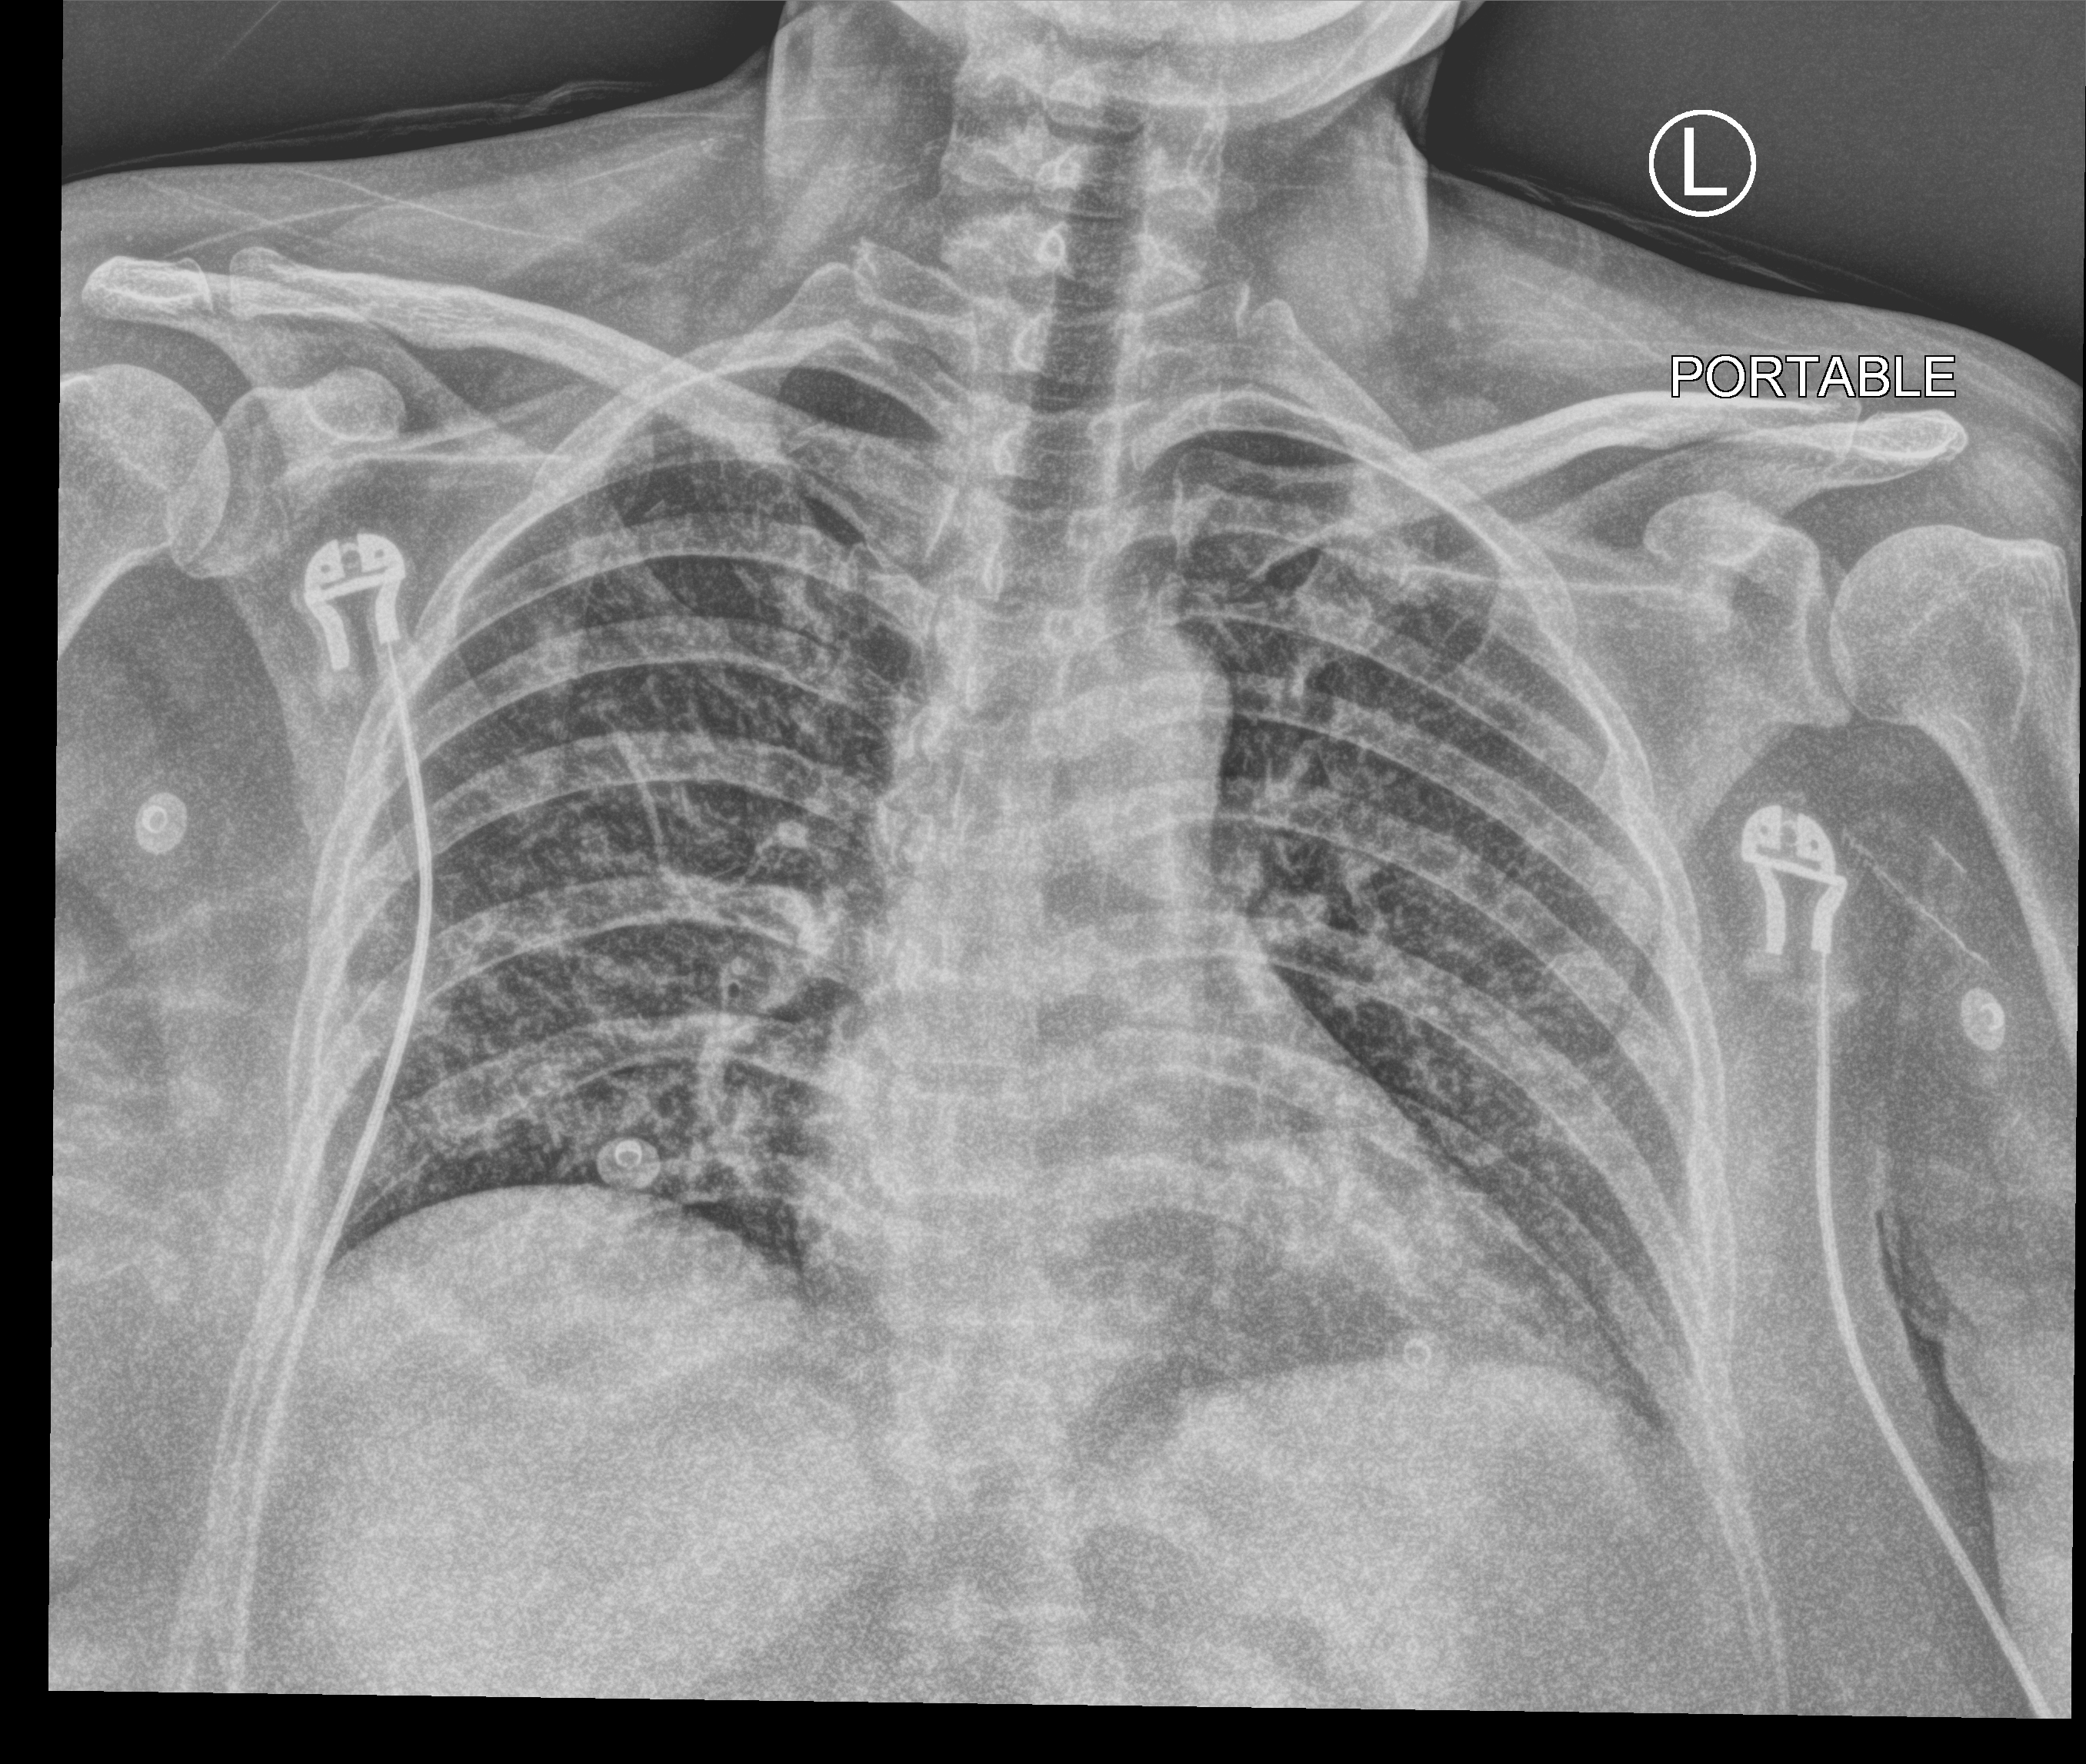
Bedside chest radiograph (computed radiography); anteroposterior (AP) projection. Patient hospitalised with COVID-19; female, aged 18–59 years.
Hospital-stay facts (about this admission, not read from this image; timing relative to this image not recorded):
- admitted to intensive care during this hospital stay: no